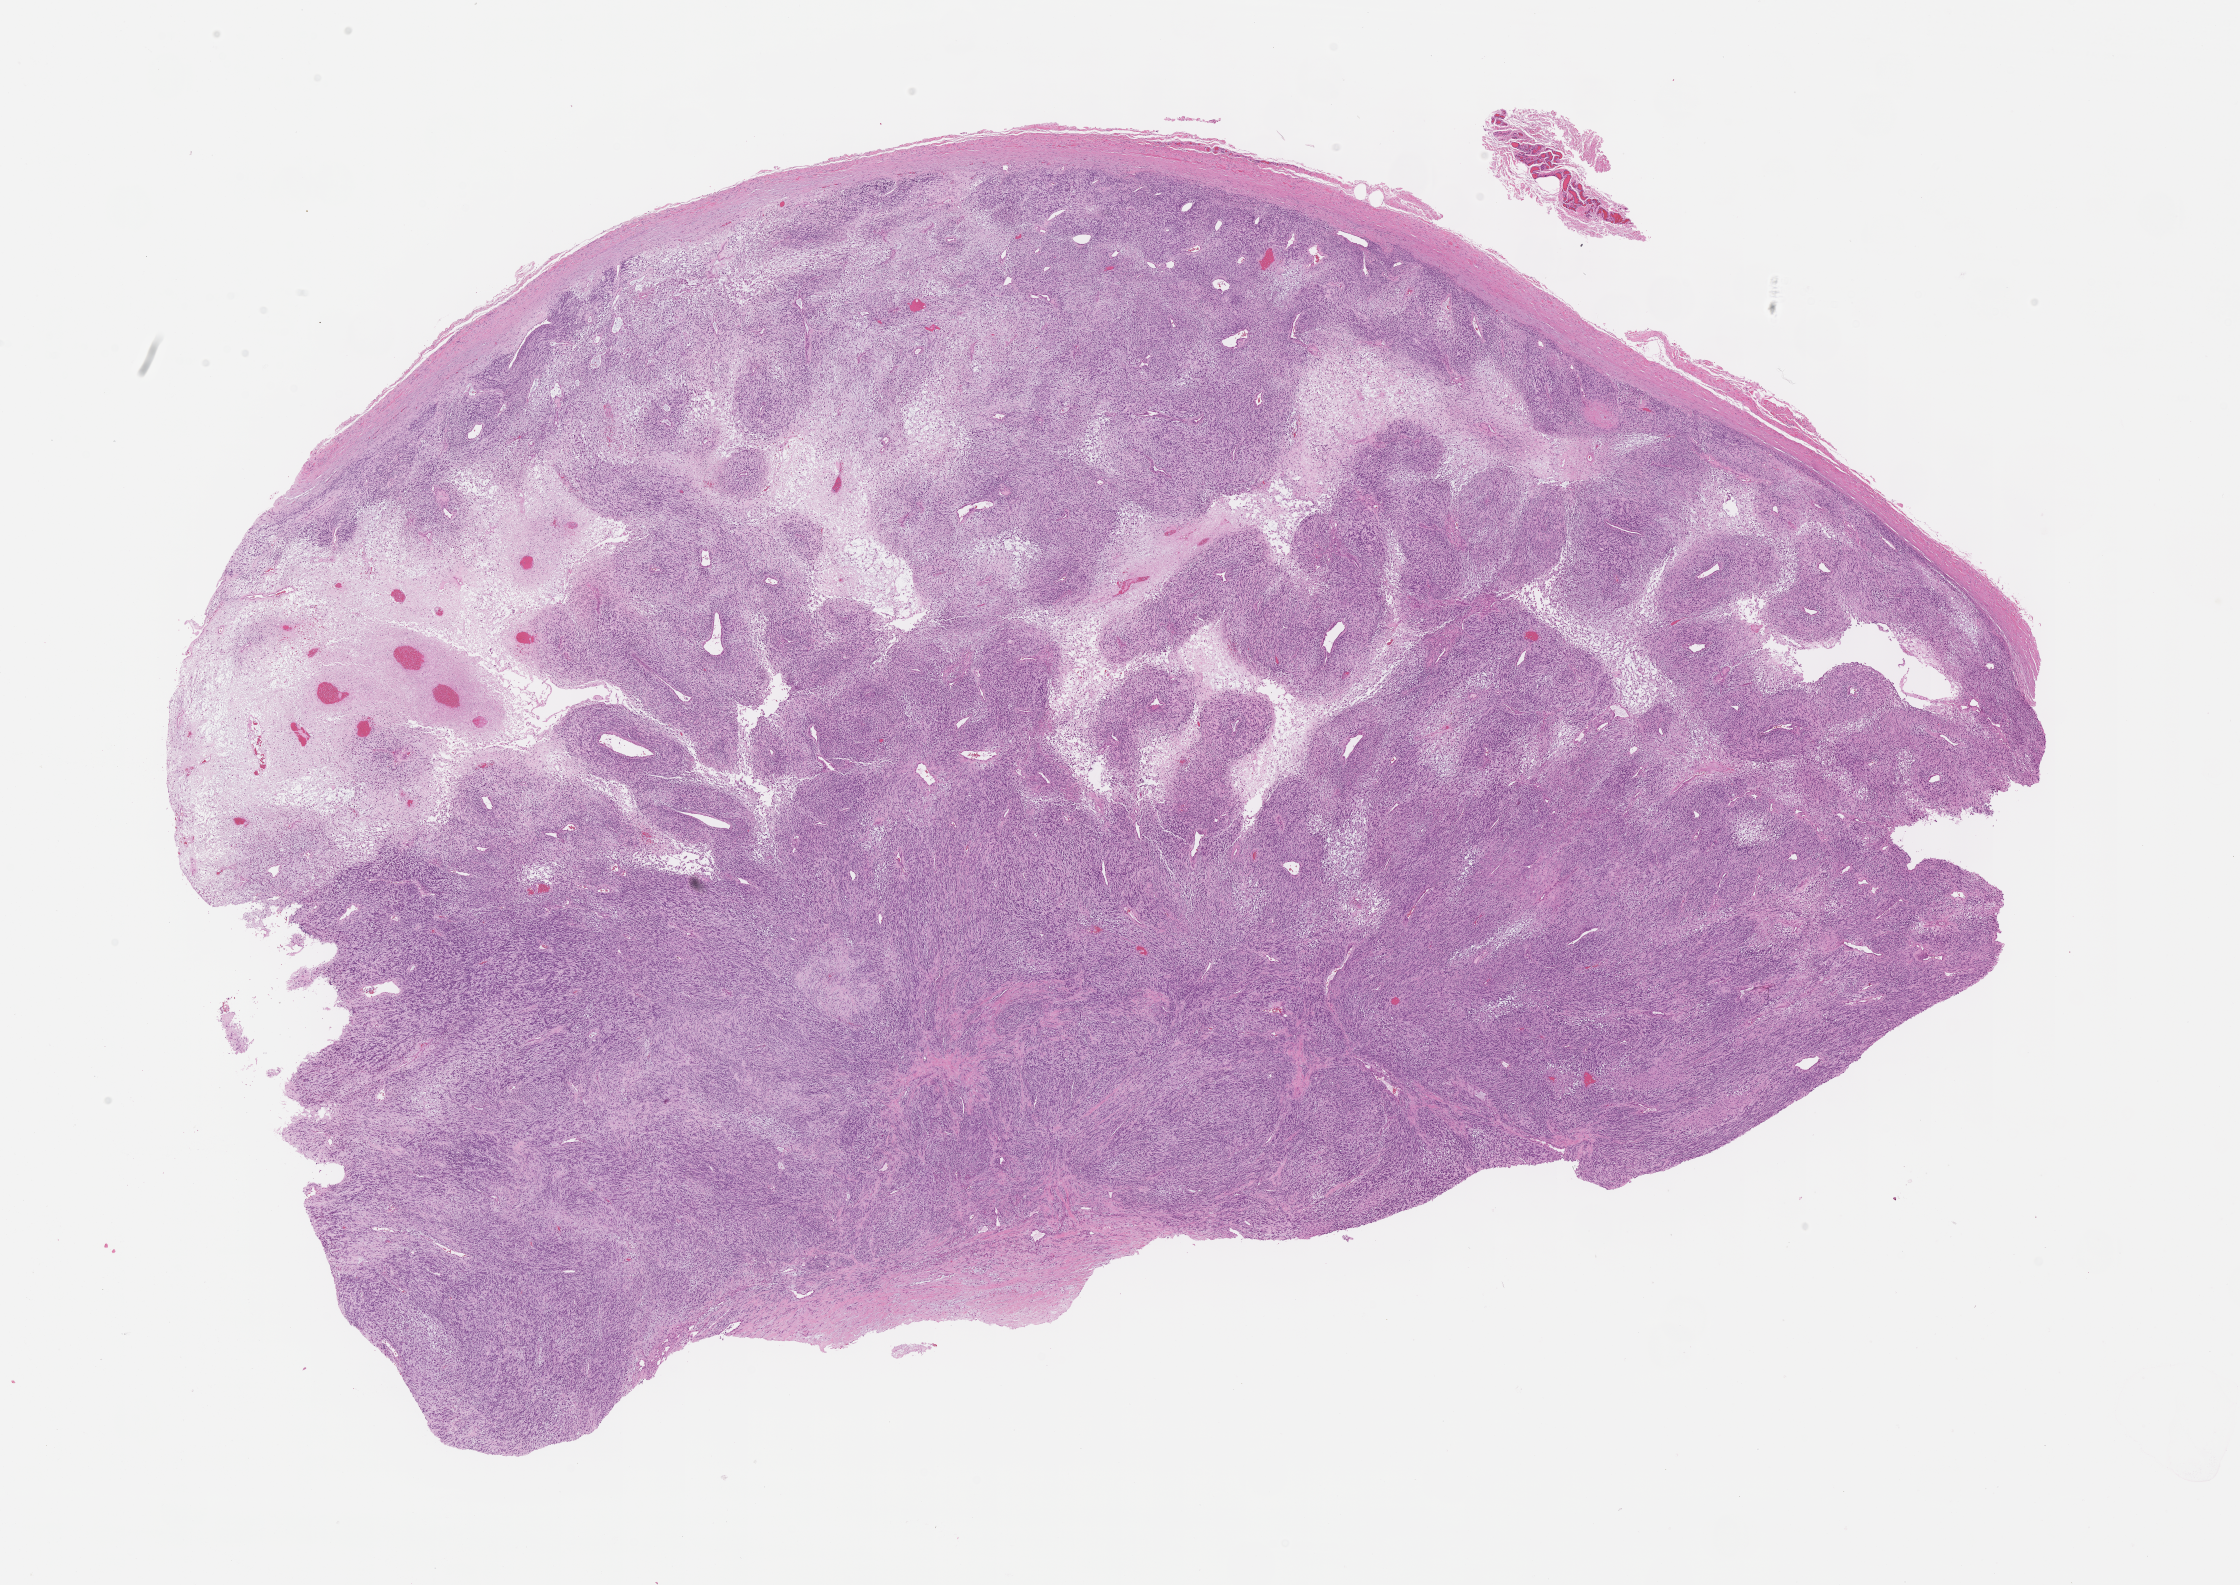
Hematoxylin and eosin (H&E) whole-slide image of tumor tissue — shown as a low-resolution overview of the whole scanned area (about 18.1 x 12.8 mm), FFPE section, site: scrotum, left. Male patient, age at diagnosis 2.4 years.
Diagnosis: rhabdomyosarcoma; histological classification: embryonal rhabdomyosarcoma.